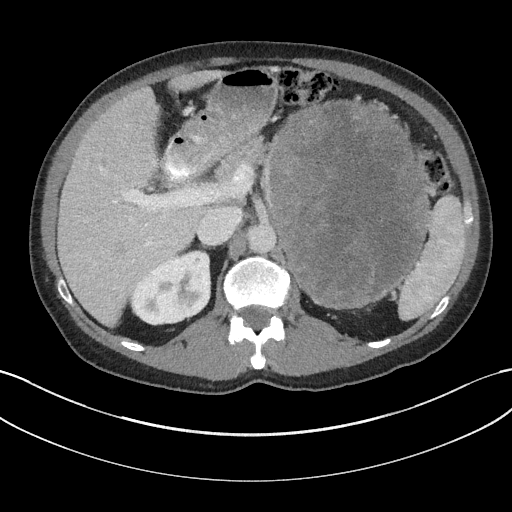
Contrast-enhanced abdominal CT, one axial slice; position 111 of 147 along the scan axis; reconstruction kernel I31f/3; intravenous contrast given; soft-tissue window (W 400 / L 40 HU); 512 × 512 image matrix. Male patient, age 58 years. Case-level facts recorded for this patient, not image findings: diagnosis: adrenocortical carcinoma; tumour side: left adrenal; tumour size at pathology: 22 cm; Ki-67 index: 26 %; stage (as recorded): 2.
Annotated regions visible in this slice (semi-automatic segmentation, software-assisted and operator-edited):
- mass: bounding box (x1, y1, x2, y2) in pixels: (271, 103, 427, 305)